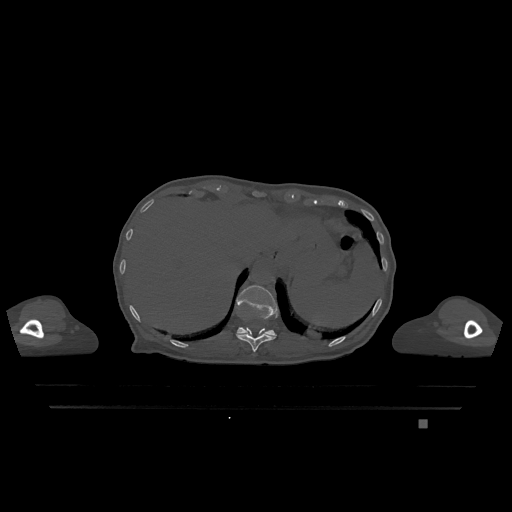
CT including the spine, one axial slice. Slice 567 of 1317 in the series (ordered by position). Bone window (W 1800 / L 400 HU). 0.5 mm slice thickness. 512 × 512 image matrix, field of view 500 × 500 mm. Patient: female, 74 years. Case-level facts recorded for this patient, not image findings: primary cancer: lung; vertebrae with lytic lesions (as recorded): T1, T4, T5, T6, L4, L5.
Outlined on this slice (semi-automatically segmented with operator editing):
- T11 vertebra: bounding box (x1, y1, x2, y2) in pixels: (236, 328, 276, 352)
- T12 vertebra: (237, 285, 278, 337)